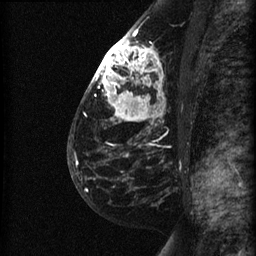
Breast MRI (dynamic contrast-enhanced), one sagittal slice; slice 40 of 60 in the series (ordered by position); dynamic contrast-enhanced series, image 2 of 3 at this slice position (ordered by acquisition); 1.5 T; TE 4.2 ms, TR 22.7 ms; 1.5 mm slice thickness; 256 × 256 image matrix, field of view 180 × 180 mm. Patient: female, 48 years. From the clinical record (not read from this slice): setting: breast cancer imaged before/during neoadjuvant chemotherapy; receptor status: triple-negative.
Outlined on this slice (semi-automatic segmentation, software-assisted and operator-edited):
- analysis volume of interest (the breast-tissue region the enhancement analysis was run in; not a lesion): box from (x=89, y=27) to (x=164, y=180) px
- tumour enhancement mask (voxels above the 90 % enhancement threshold inside the analysis volume of interest): (x=93, y=29)–(x=161, y=118)